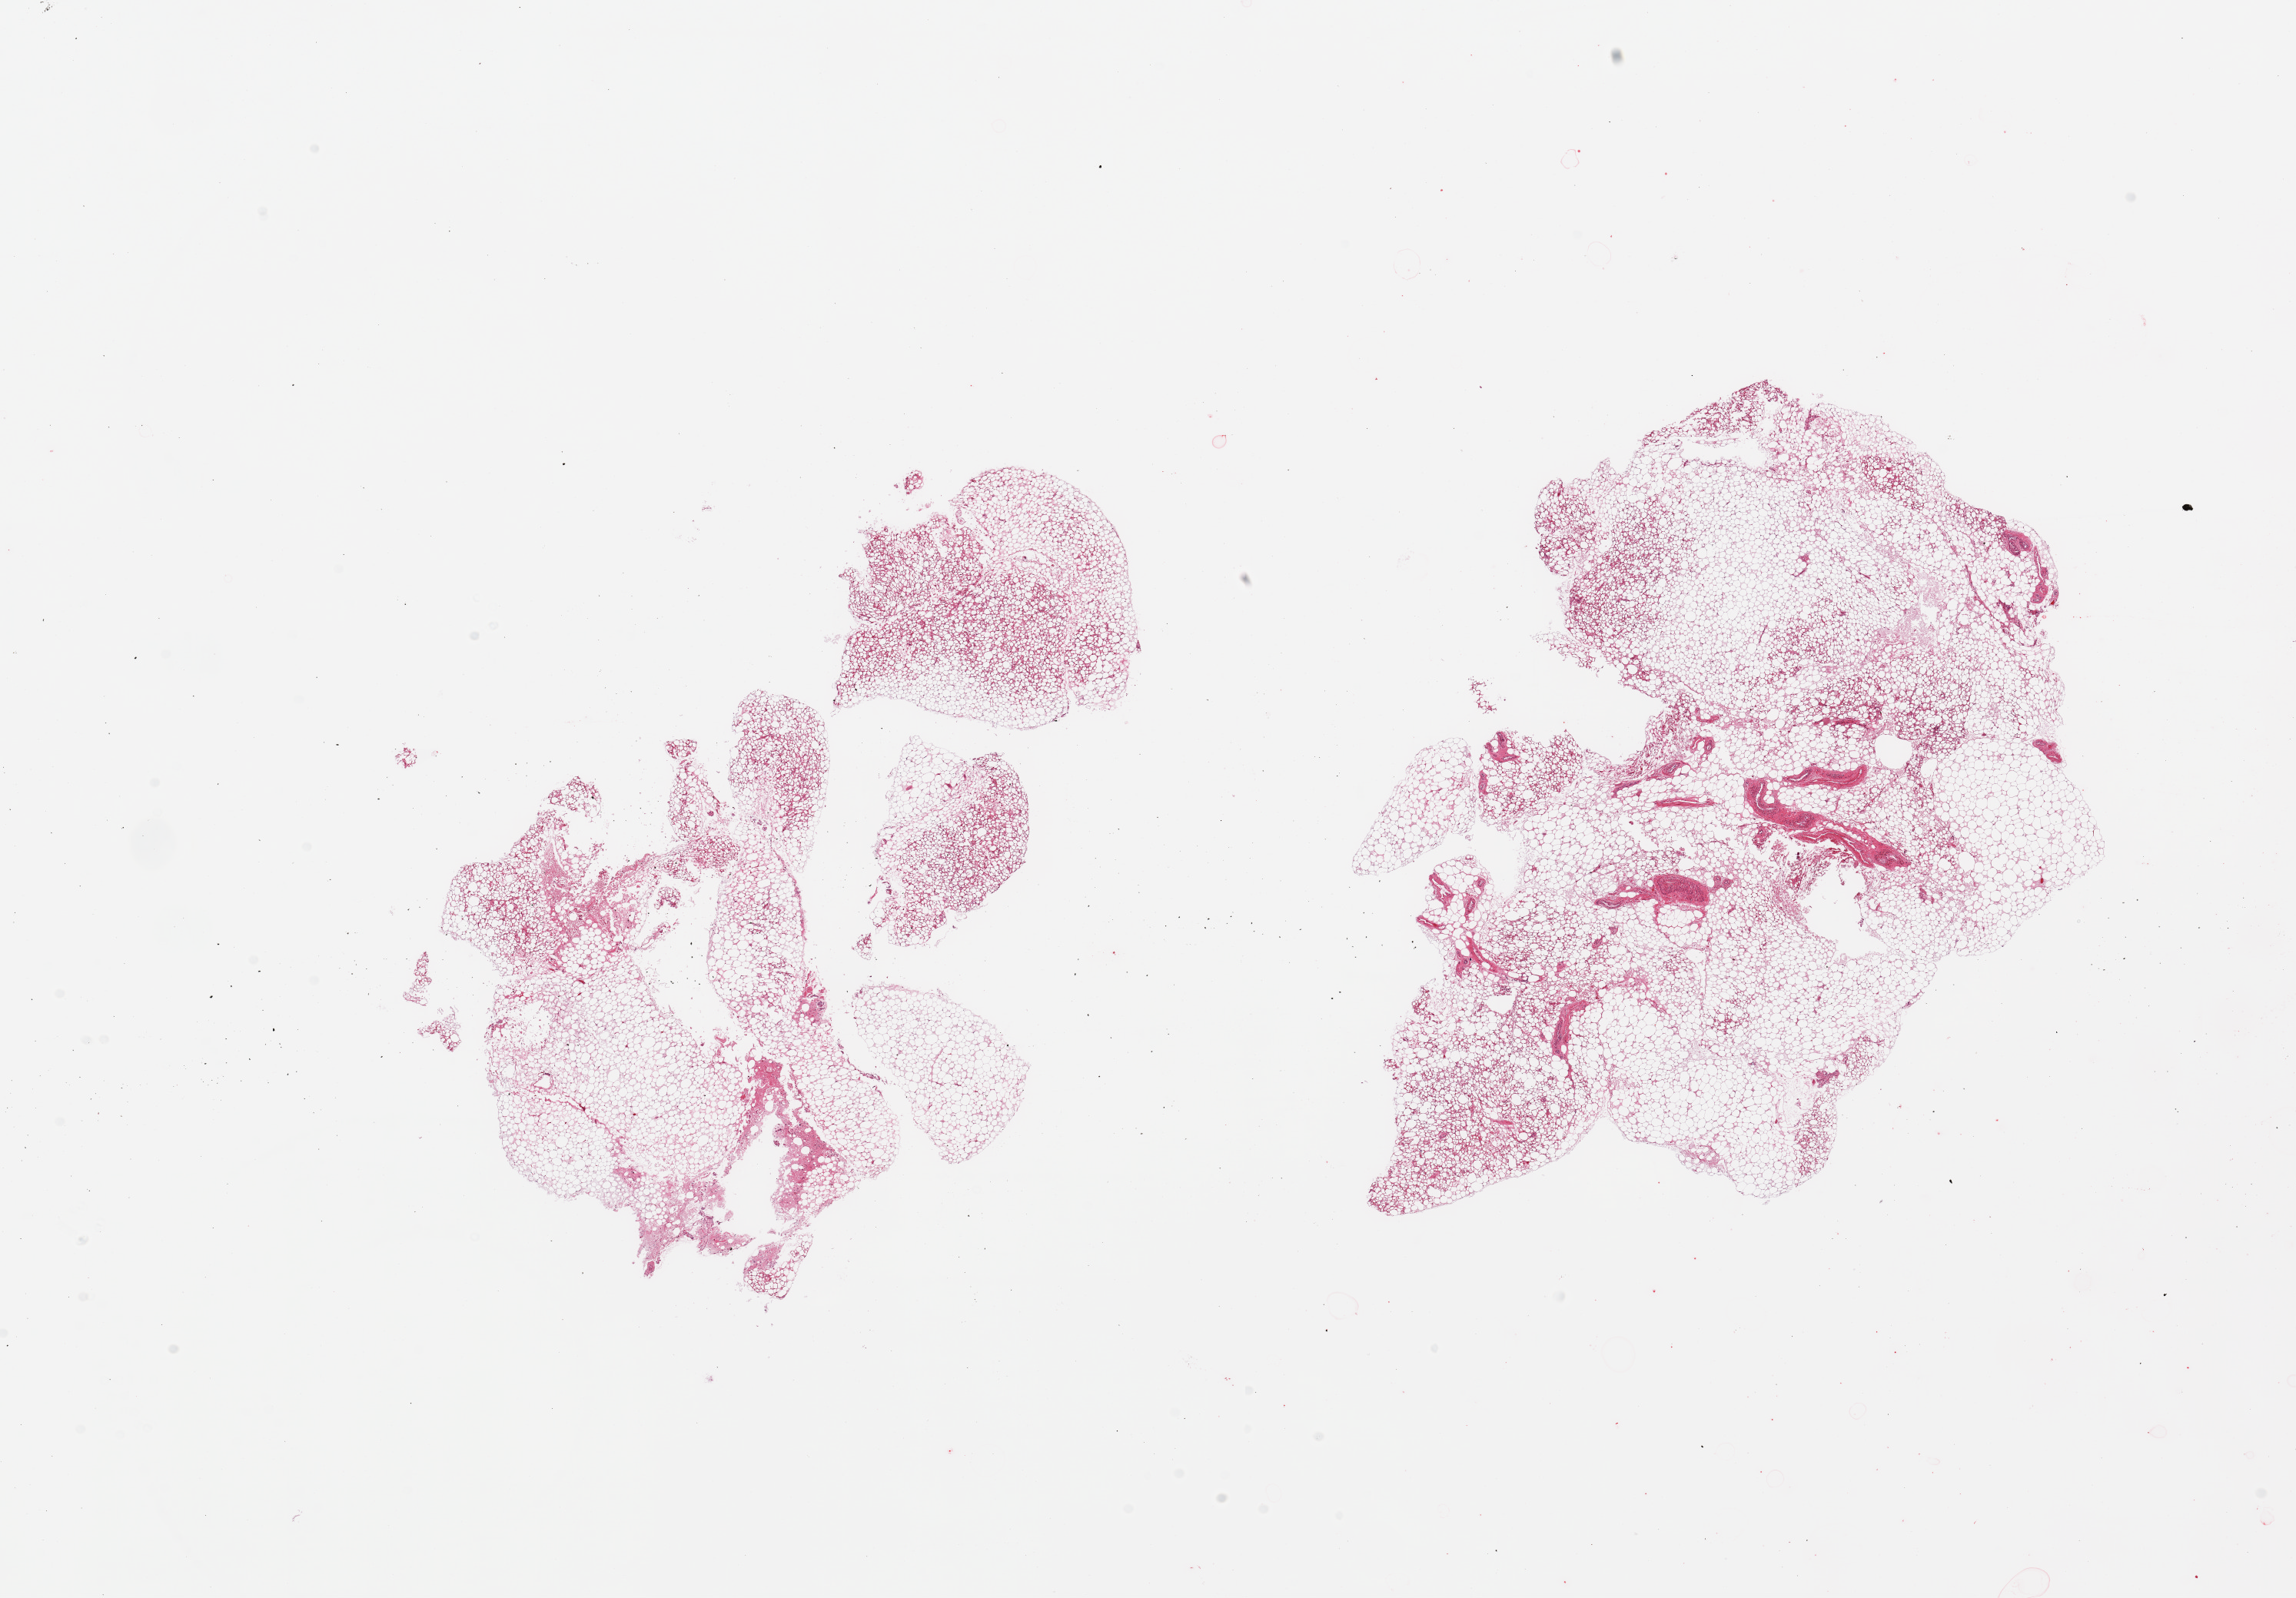
Hematoxylin and eosin (H&E) whole-slide image, brightfield, shown as a low-resolution overview of the whole scanned area (about 23.6 x 16.4 mm, from a 20x scan). PAXgene-fixed, paraffin-embedded tissue. Target tissue: adrenal gland. Tissue donor sample.
* review note (as recorded): 2 pieces; all adipose tissue; no obvious adrenal cells